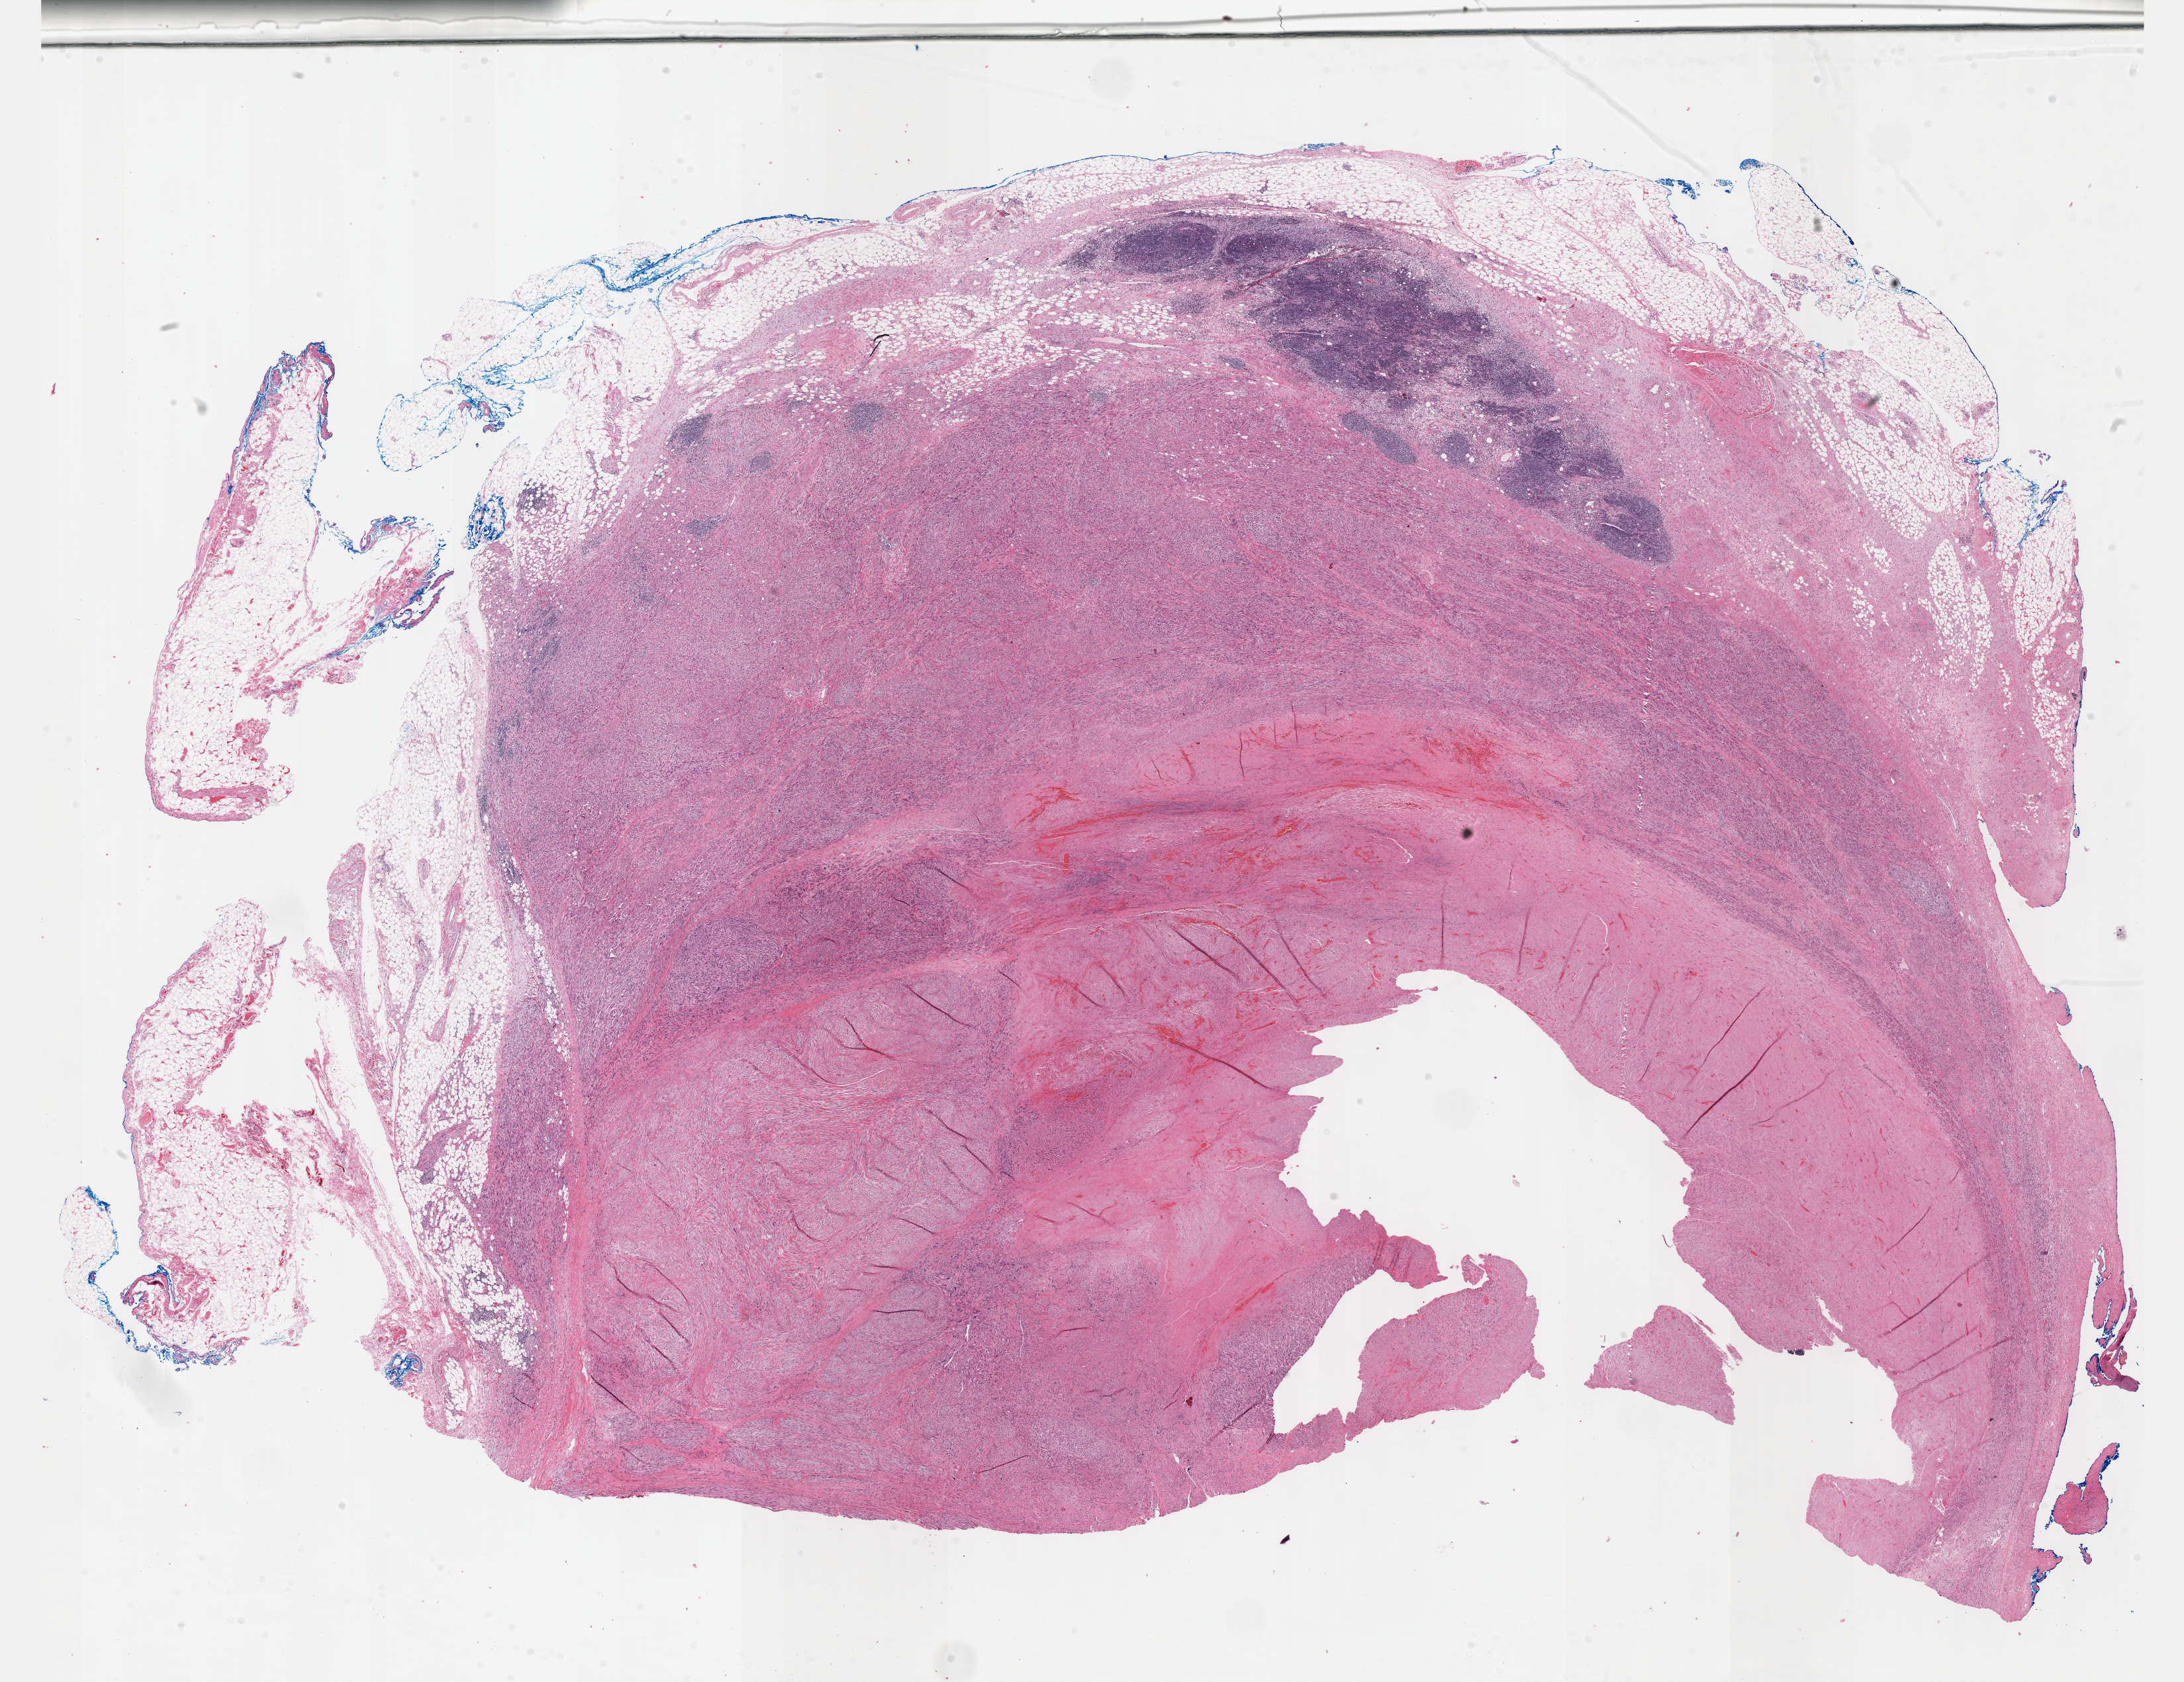
Whole-slide histology image, Hematoxylin and eosin (H&E) stained, shown as a low-resolution overview of the whole scanned area (about 26.7 x 20.5 mm), FFPE section, primary tumour sample from the connective, subcutaneous and other soft tissues. Female patient.
Diagnosis: Leiomyosarcoma, NOS.